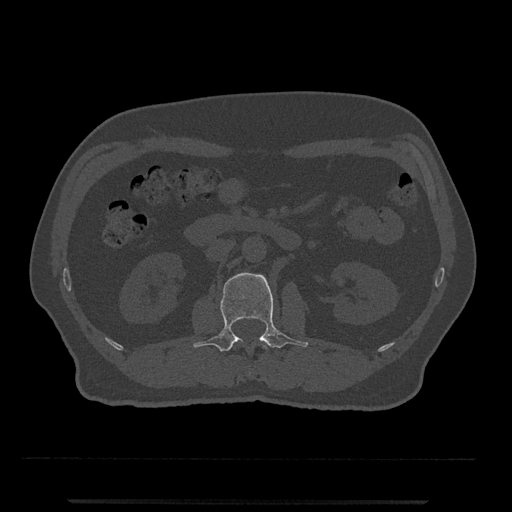
CT including the spine, one axial slice; slice 277 of 797 in the series (ordered by position); reconstruction kernel Br40s/3; bone window (W 1800 / L 400 HU); 0.5 mm slice thickness; 512 × 512 image matrix. Male patient, age 63 years. Case-level facts recorded for this patient, not image findings: primary cancer: prostate.
Structures marked on this image (semi-automatic segmentation, software-assisted and operator-edited):
- L1 vertebra: bounding box (x1, y1, x2, y2) in pixels: (259, 339, 268, 350)
- L2 vertebra: (193, 272, 308, 352)